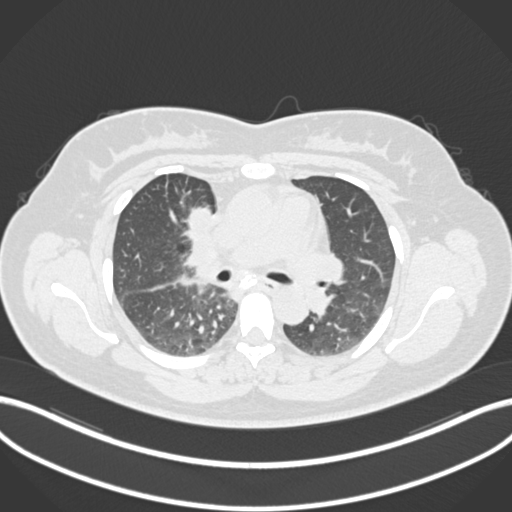
Chest CT, one axial slice. Position 105 of 183 along the scan axis. Lung window (W 1500 / L -600 HU). 512 × 512 image matrix. Female patient, age 46 years. From the clinical record (not read from this slice): clinical TNM (as recorded): T2a N1 M0.
Annotated regions visible in this slice (rectangle marked by the reading radiologist):
- lung tumour (recorded histology: adenocarcinoma): bounding box <182,205,211,236> (left, top, right, bottom; pixels)